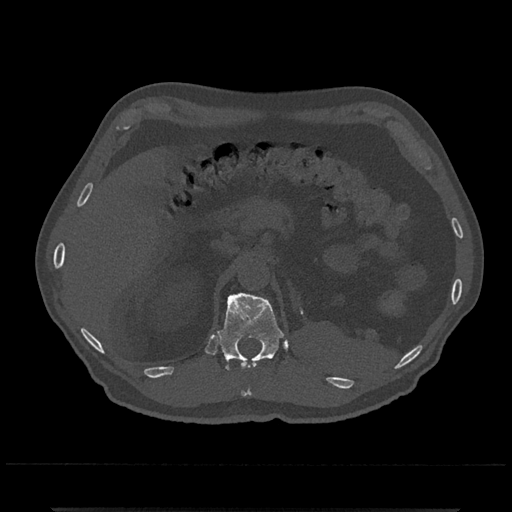
CT including the spine, one axial slice. Slice 443 of 797 in the series (ordered by position). Reconstruction kernel Br40s/3. 120 kVp. Bone window (W 1800 / L 400 HU). 0.5 mm slice thickness. 512 × 512 image matrix, field of view 393 × 393 mm. Male patient, age 67 years. From the clinical record (not read from this slice): primary cancer: prostate.
Outlined on this slice (semi-automatic segmentation, software-assisted and operator-edited):
- T11 vertebra: bounding box <242,361,256,396> (left, top, right, bottom; pixels)
- T12 vertebra: <217,292,284,371>